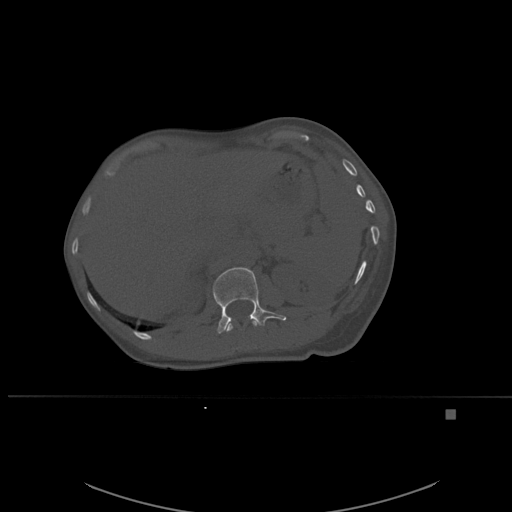
CT including the spine, one axial slice; bone window (W 1800 / L 400 HU); 1.5 mm slice thickness; 512 × 512 image matrix, field of view 440 × 440 mm. Patient: female, 45 years. From the clinical record (not read from this slice): primary cancer: lung.
Outlined on this slice (semi-automatic segmentation, software-assisted and operator-edited):
- L1 vertebra: bounding box [x1, y1, x2, y2] px = [213, 267, 286, 334]
- T12 vertebra: [224, 320, 261, 332]